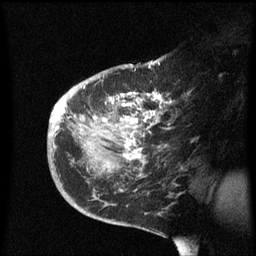
Breast MRI (dynamic contrast-enhanced), one sagittal slice; slice 37 of 60 in the series (ordered by position); dynamic contrast-enhanced series, image 2 of 3 at this slice position (ordered by acquisition); 1.5 T; TE 4.2 ms, TR 8.4 ms; 2.3 mm slice thickness; 256 × 256 image matrix. Female patient, age 38 years. Case-level facts recorded for this patient, not image findings: setting: breast cancer imaged before/during neoadjuvant chemotherapy; receptor status: HER2-positive.
Annotated regions visible in this slice (semi-automatically segmented with operator editing):
- analysis volume of interest (the breast-tissue region the enhancement analysis was run in; not a lesion): box from (x=47, y=78) to (x=189, y=213) px
- tumour enhancement mask (voxels above the 70 % enhancement threshold inside the analysis volume of interest): (x=67, y=92)–(x=172, y=163)